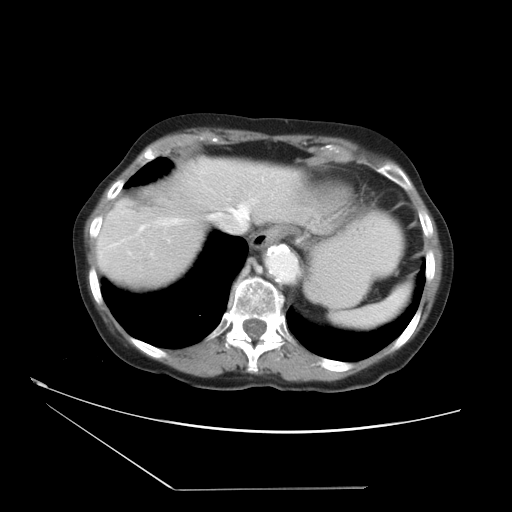
Contrast-enhanced abdominal CT, one axial slice. Slice 30 of 36 in the series (ordered by position). 120 kVp. Soft-tissue window (W 400 / L 40 HU). 5 mm slice thickness. 512 × 512 image matrix, field of view 384 × 384 mm. Female patient, age 81 years. Case-level facts recorded for this patient, not image findings: diagnosis: colorectal cancer liver metastases, imaged before liver resection; multiple liver metastases: no; largest metastasis: 1.6 cm.
Outlined on this slice (manually delineated by an expert):
- hepatic veins: bounding box [x1, y1, x2, y2] px = [161, 203, 249, 225]
- liver: [95, 159, 322, 289]
- planned liver remnant (the part of the liver to remain after resection): [96, 159, 319, 289]